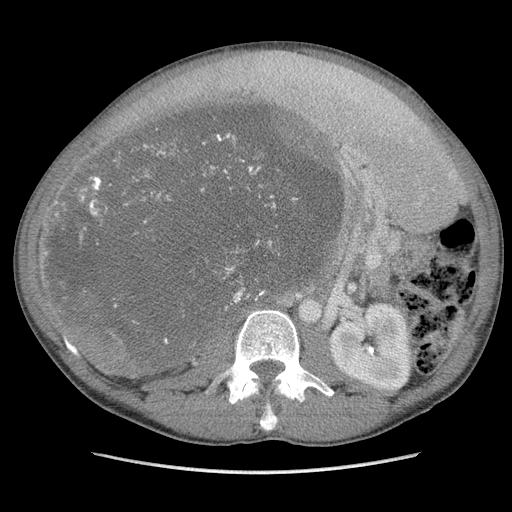
Contrast-enhanced abdominal CT, one axial slice. Position 58 of 115 along the scan axis. Soft-tissue window (W 400 / L 40 HU). 5 mm slice thickness. 512 × 512 image matrix, field of view 360 × 360 mm. Male patient. Case-level facts recorded for this patient, not image findings: diagnosis: adrenocortical carcinoma; tumour side: right adrenal; Ki-67 index: 13 %; stage (as recorded): 3.
Structures marked on this image (semi-automatic segmentation, software-assisted and operator-edited):
- mass: bounding box (x1, y1, x2, y2) in pixels: (53, 101, 336, 377)